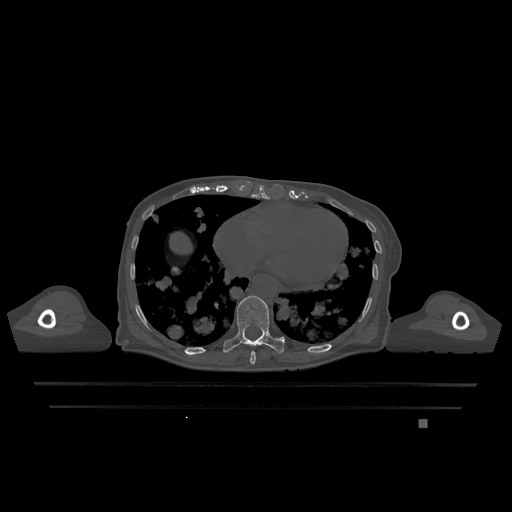
CT including the spine, one axial slice; position 650 of 1317 along the scan axis; bone window (W 1800 / L 400 HU); 0.5 mm slice thickness; 512 × 512 image matrix, field of view 500 × 500 mm. Female patient, age 74 years. From the clinical record (not read from this slice): primary cancer: lung; vertebrae with lytic lesions (as recorded): T1, T4, T5, T6, L4, L5.
Annotated regions visible in this slice (semi-automatically segmented with operator editing):
- T10 vertebra: bounding box <223,295,284,354> (left, top, right, bottom; pixels)
- T9 vertebra: <250,351,256,364>